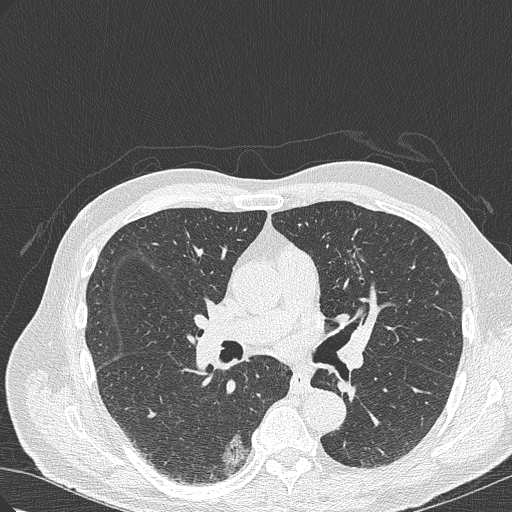
Chest CT (low-dose screening protocol), one axial image, baseline screening round, lung window (W 1500 / L -600 HU), 1 mm slice thickness, lung (sharp) reconstruction kernel (B50f), 120 kVp, 512 × 512 image matrix. Male, age 70 years at enrolment. Current smoker at enrolment.
Expert-annotated lung lesion, bounding box [x1, y1, x2, y2] px = [198, 419, 261, 477]. The screening reader recorded 4 non-calcified nodules or masses ≥4 mm on this exam; which of them this box marks is not recorded. Official screen result: positive, change unspecified: nodule(s) >= 4 mm or enlarging nodule(s), mass(es), or other non-specific abnormalities suspicious for lung cancer. Later outcome: lung cancer diagnosed 978 days after this screen (after the third annual screen) — bronchiolo-alveolar adenocarcinoma, NOS, right lower lobe, poorly differentiated (G3), stage IB (AJCC 6th edition), 30 mm at pathology.